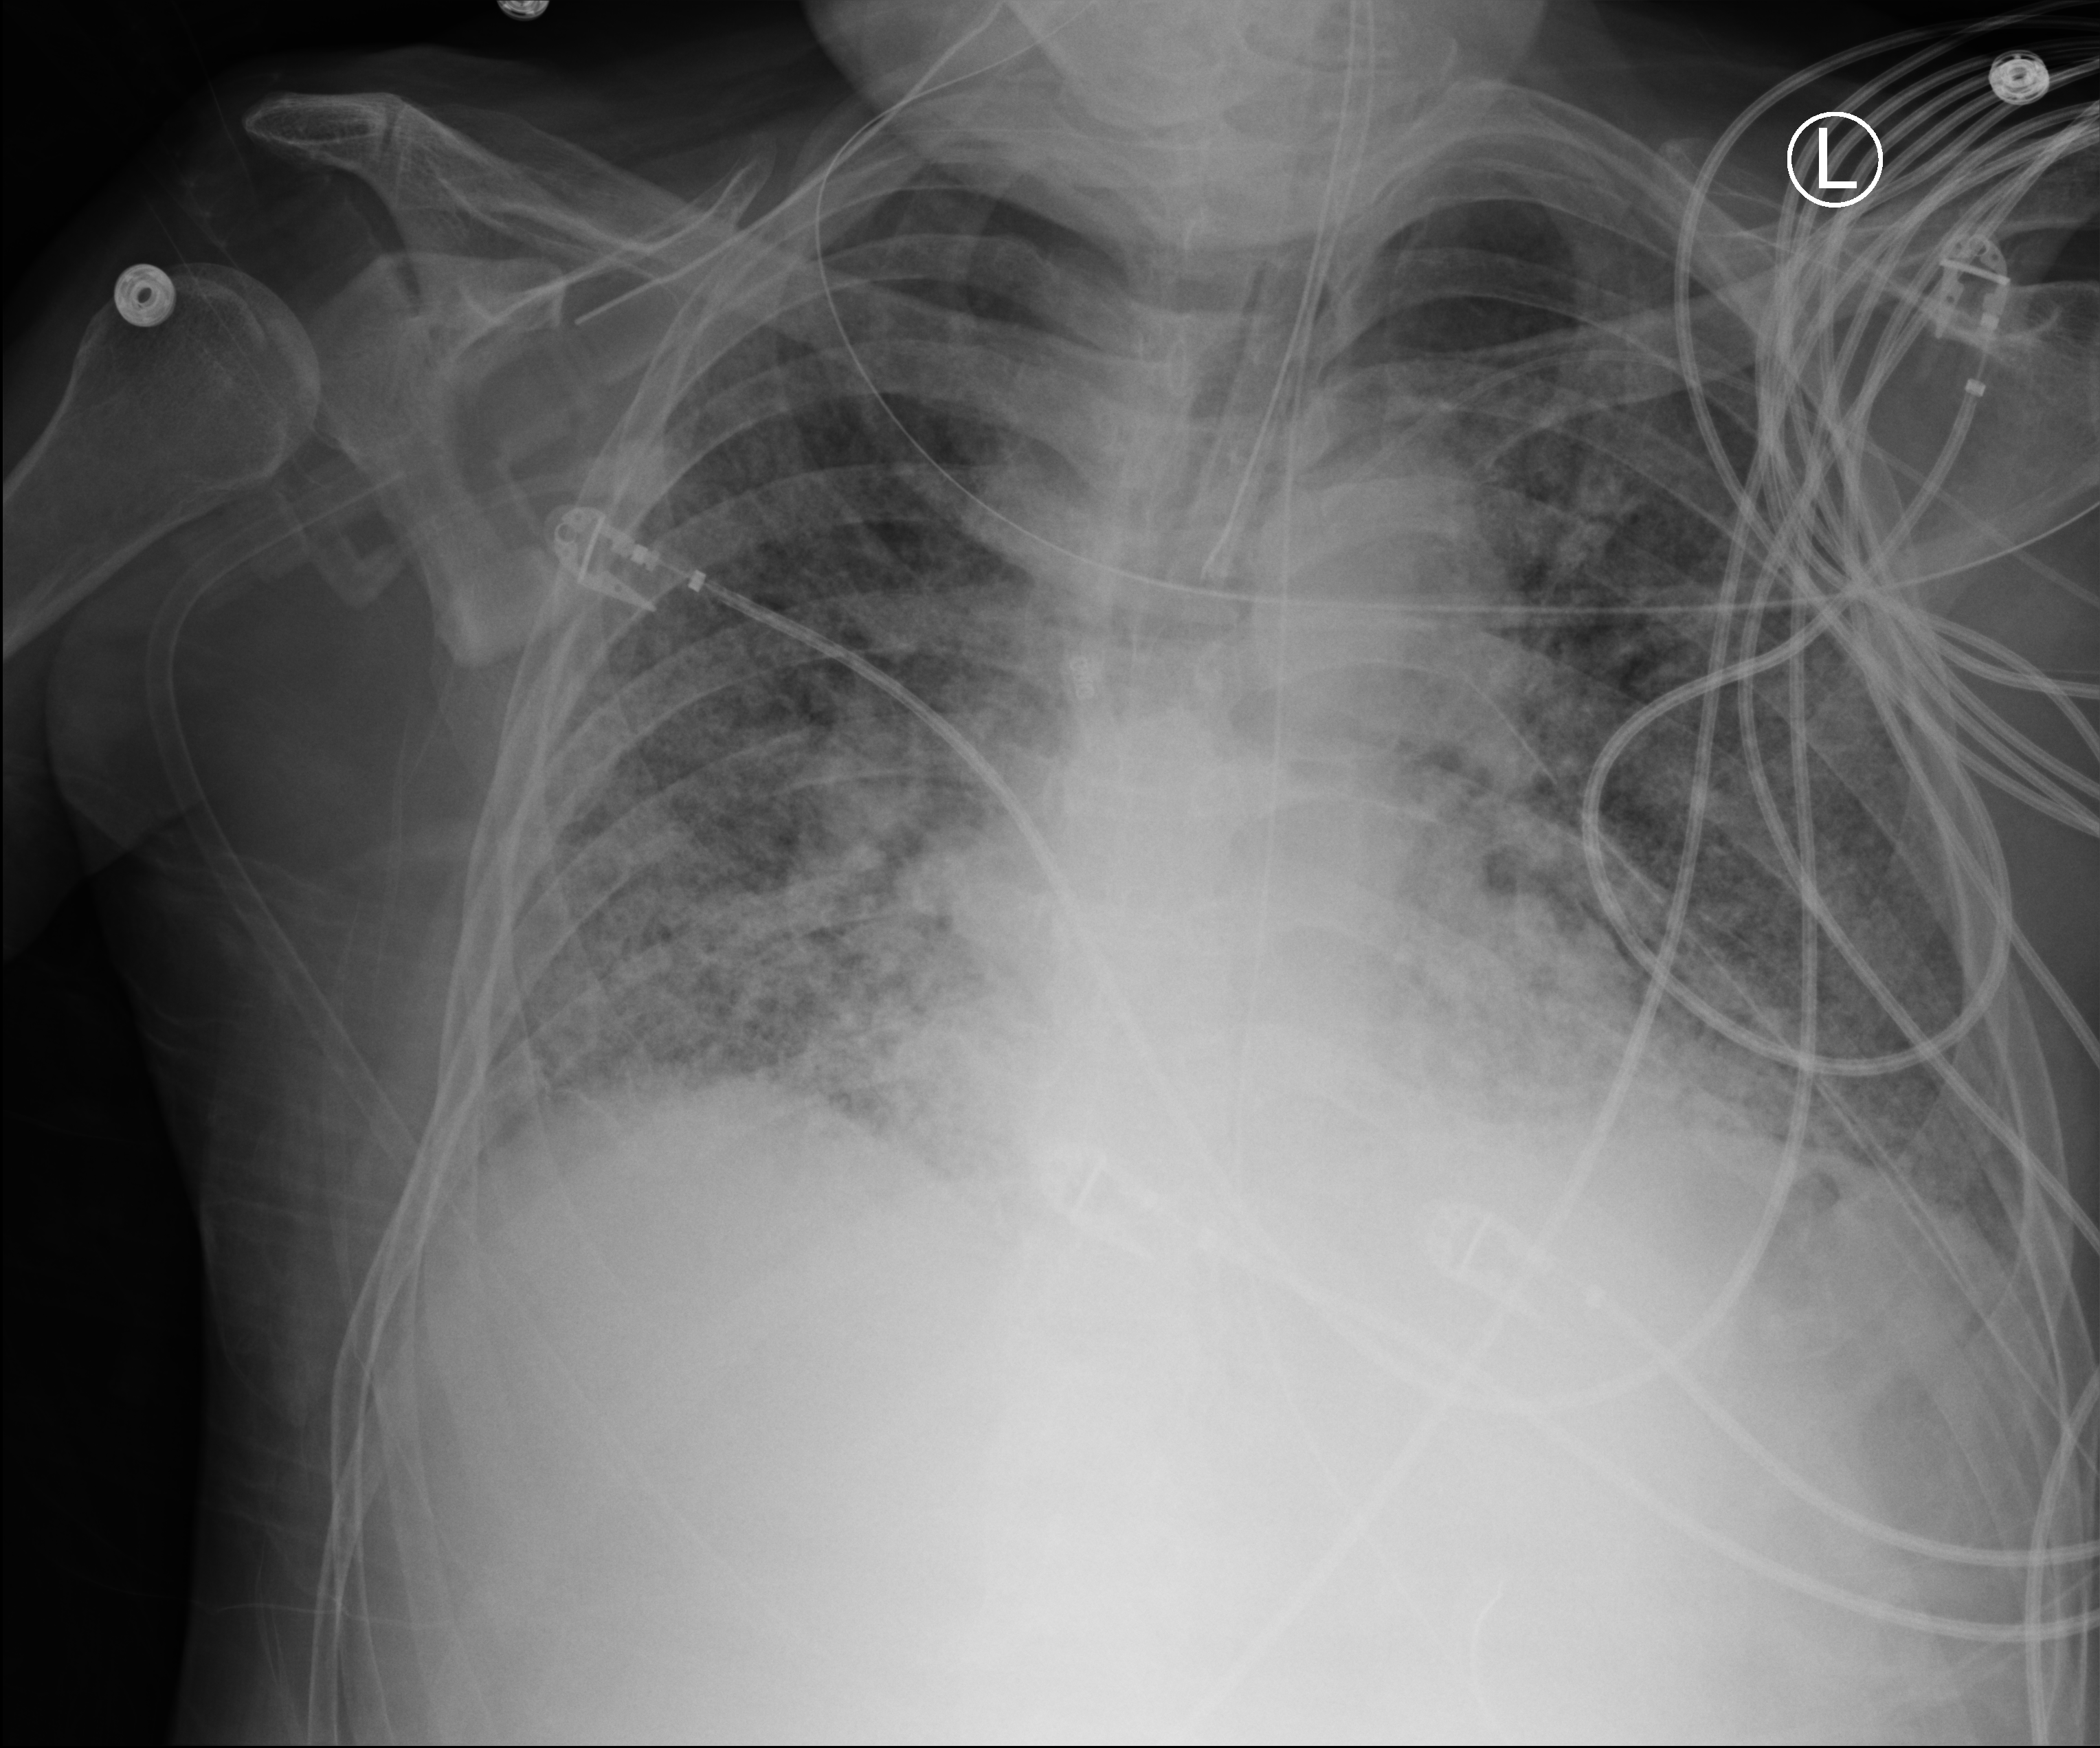
Portable chest radiograph; anteroposterior (AP) projection. Patient hospitalised with COVID-19; male, aged 60–74 years.
From the hospital-stay record, not from the radiograph (when in the stay this image was taken is not recorded):
- length of hospital stay: 54 days
- mechanically ventilated during this hospital stay: yes